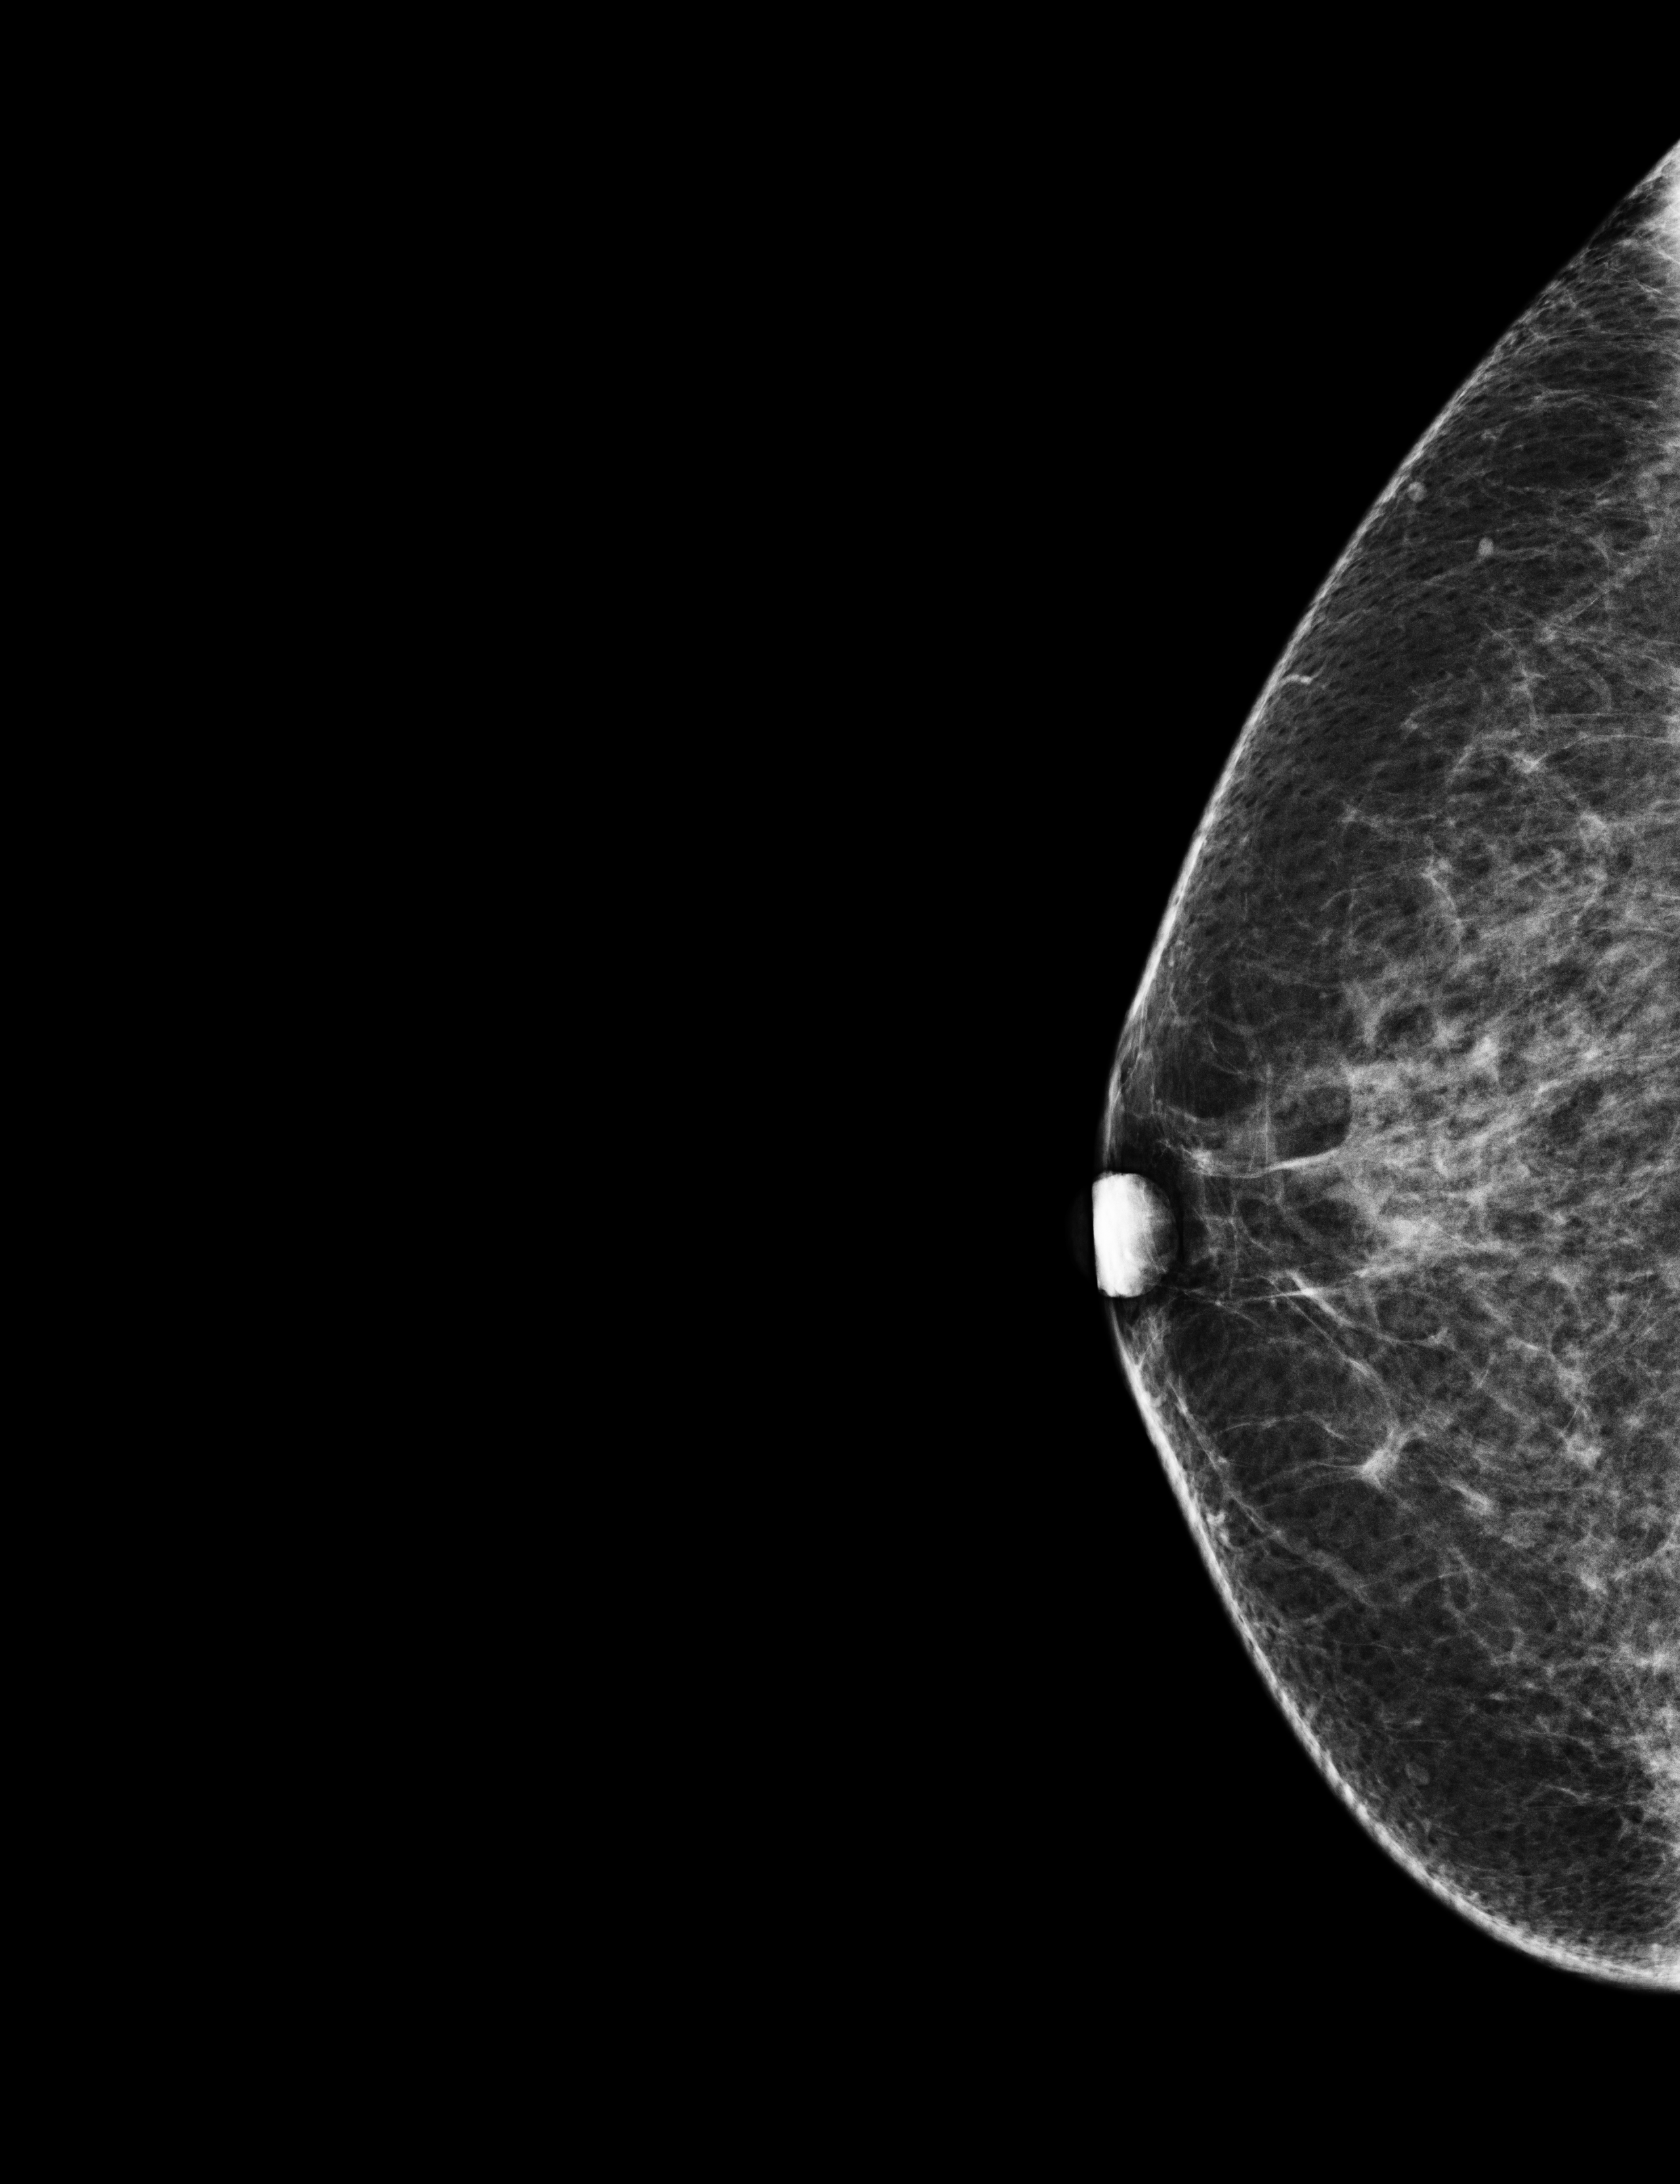
Annual screening mammography examination, system: Selenia Dimensions. Patient: female, 61 years.
Image type: full-field digital mammogram. Breast: right. Projection: cranio-caudal projection.